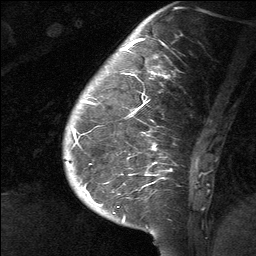
Breast MRI (dynamic contrast-enhanced), one sagittal slice. Slice 18 of 64 in the series (ordered by position). Dynamic contrast-enhanced study with each time point stored as its own series, time point 2 of 3 at this slice position (early post-contrast, ordered by acquisition time). 1.5 T. TE 4.8 ms, TR 27 ms. 2 mm slice thickness. 256 × 256 image matrix. Patient: female, 39 years. From the clinical record (not read from this slice): setting: breast cancer imaged before/during neoadjuvant chemotherapy; receptor status: HER2-positive.
Outlined on this slice (semi-automatically segmented with operator editing):
- analysis volume of interest (the breast-tissue region the enhancement analysis was run in; not a lesion): bounding box <63,40,201,217> (left, top, right, bottom; pixels)
- tumour enhancement mask (voxels above the 90 % enhancement threshold inside the analysis volume of interest): <73,40,168,217>